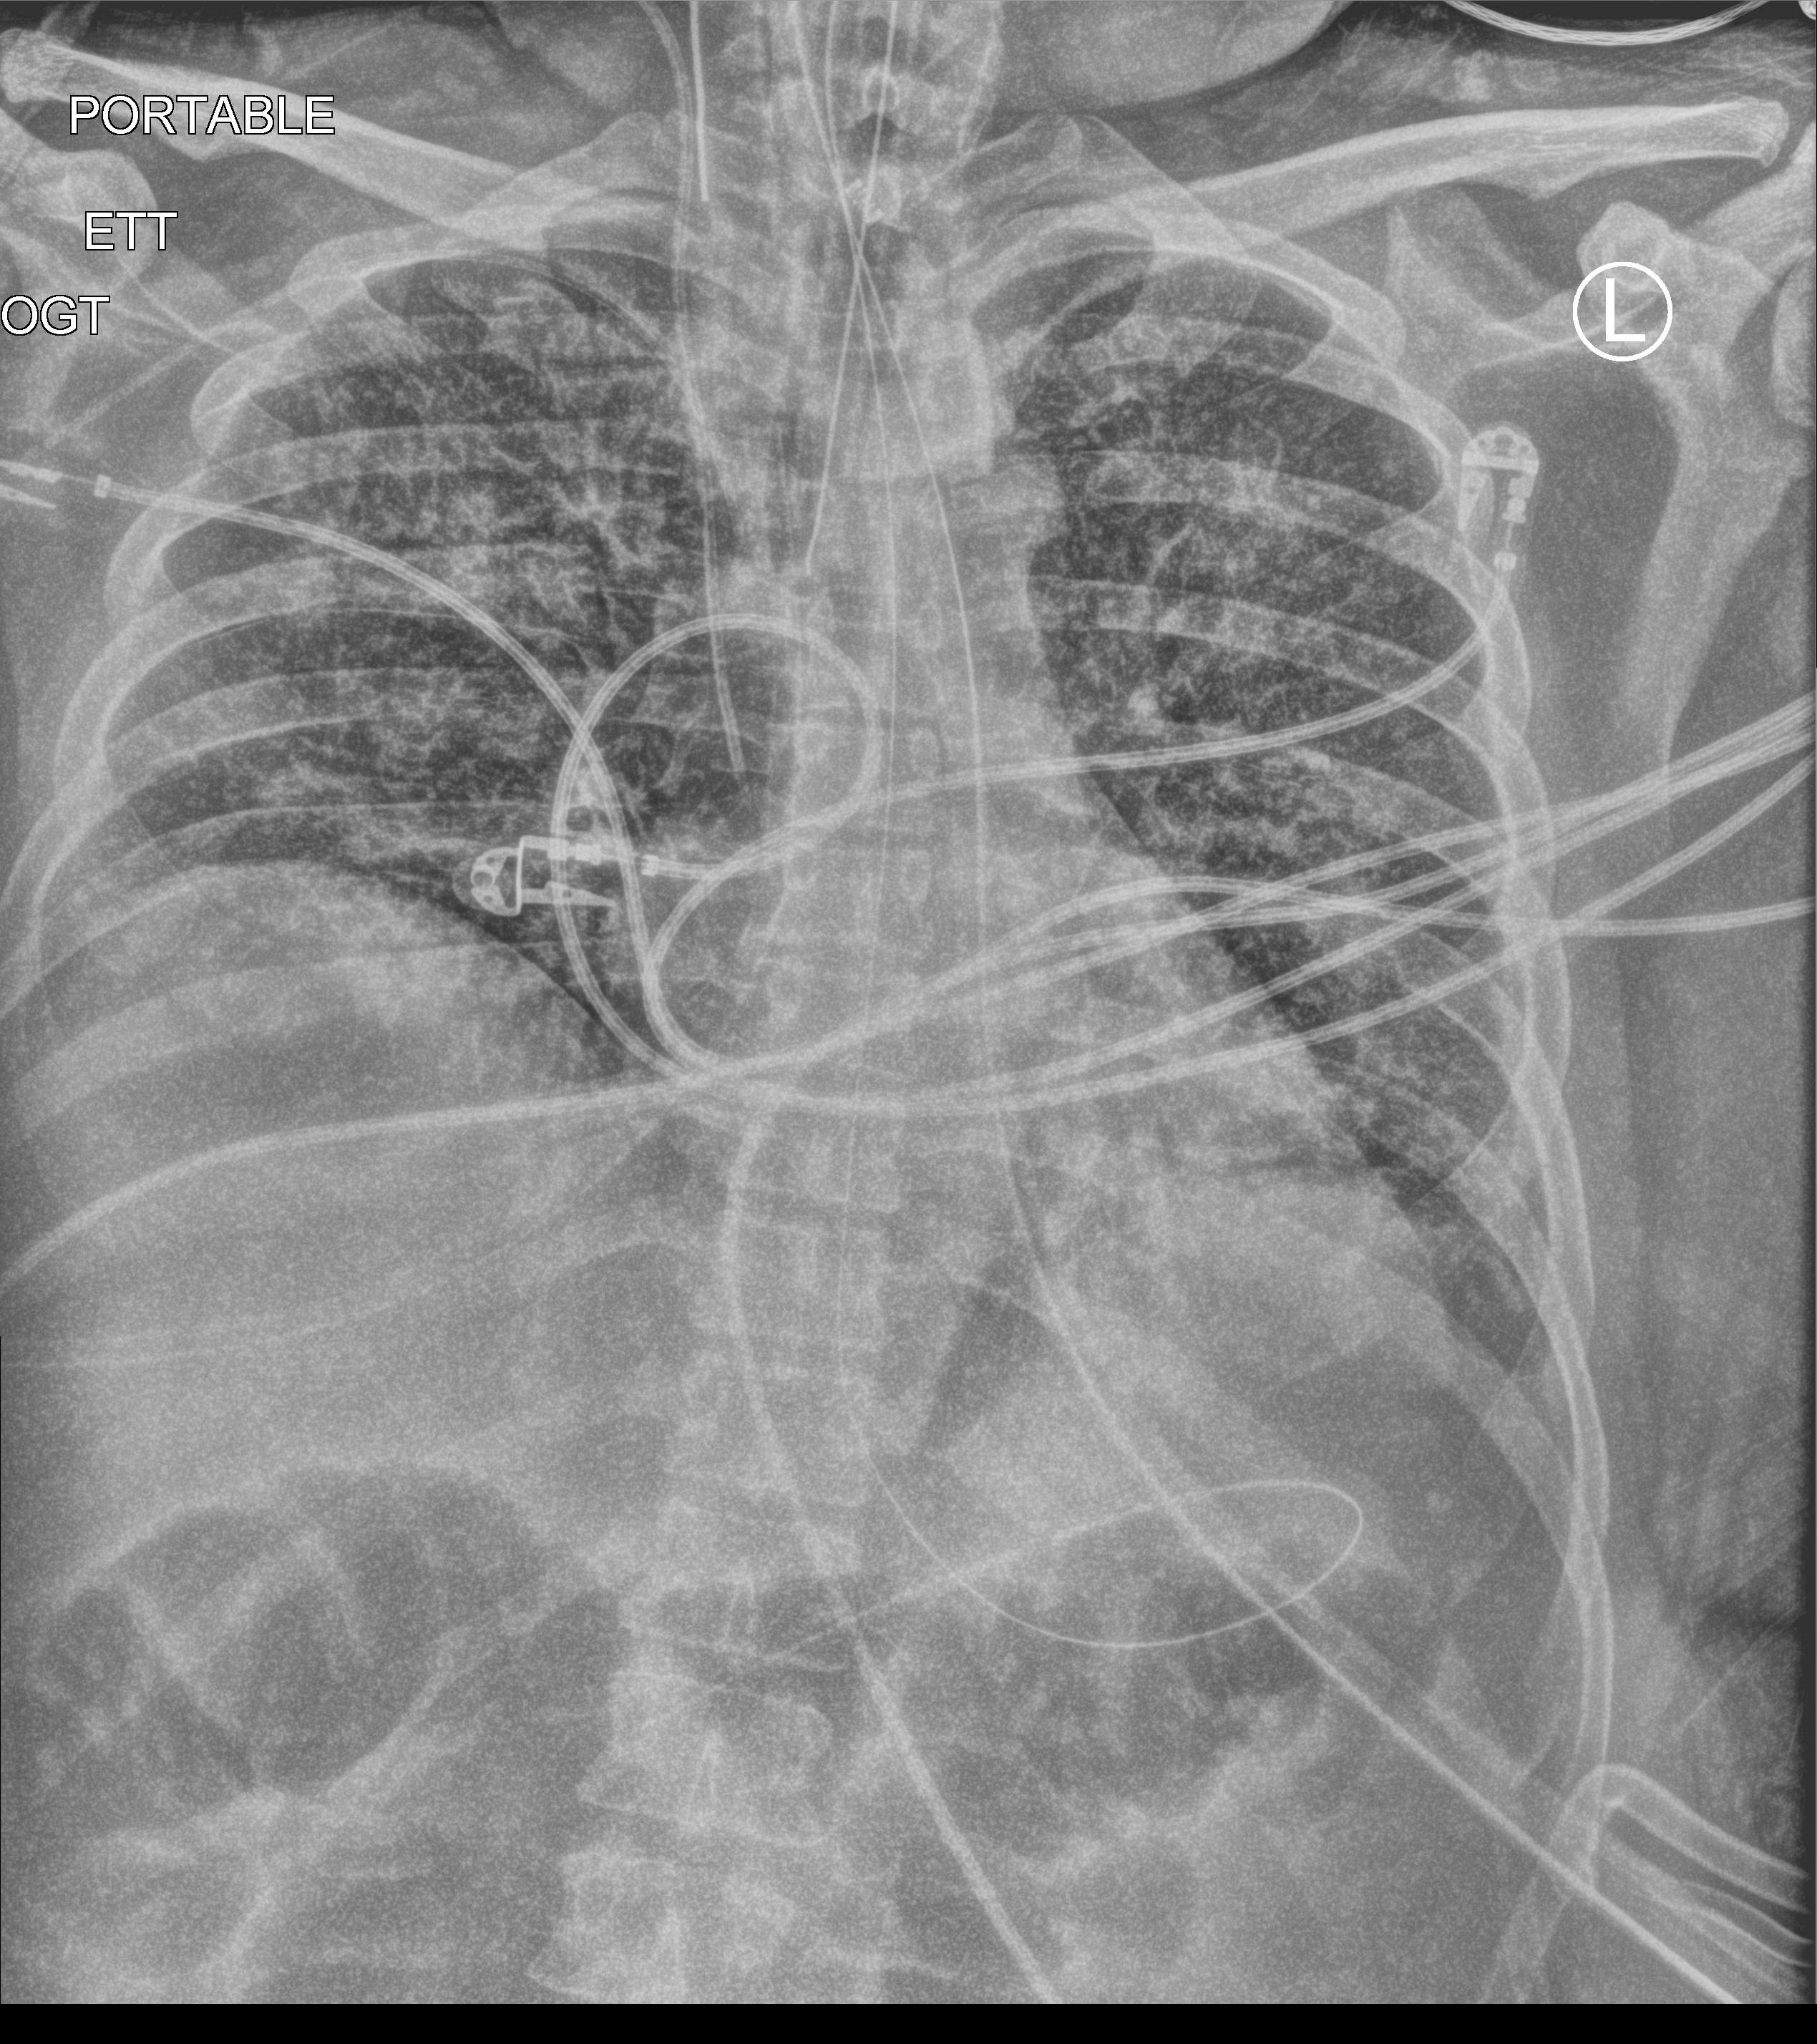
Chest X-ray (portable); anteroposterior (AP) projection. Patient hospitalised with COVID-19; male, aged 18–59 years.
From the hospital-stay record, not from the radiograph (when in the stay this image was taken is not recorded): length of hospital stay: 96 days.